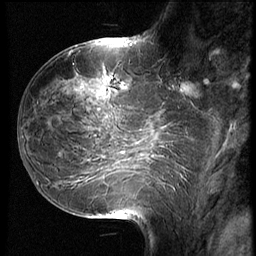
Breast MRI (dynamic contrast-enhanced), one sagittal slice; position 26 of 68 along the scan axis; 3 images stored at this slice position (order not interpretable as contrast timing); 1.5 T; TE 4.2 ms, TR 8.9 ms; 256 × 256 image matrix, field of view 200 × 200 mm. Patient: female, 39 years. Case-level facts recorded for this patient, not image findings: setting: breast cancer imaged before/during neoadjuvant chemotherapy; receptor status: HER2-positive.
Annotated regions visible in this slice (semi-automatically segmented with operator editing):
- analysis volume of interest (the breast-tissue region the enhancement analysis was run in; not a lesion): box from (x=66, y=68) to (x=141, y=127) px
- tumour enhancement mask (voxels above the 140 % enhancement threshold inside the analysis volume of interest): (x=107, y=90)–(x=111, y=93)